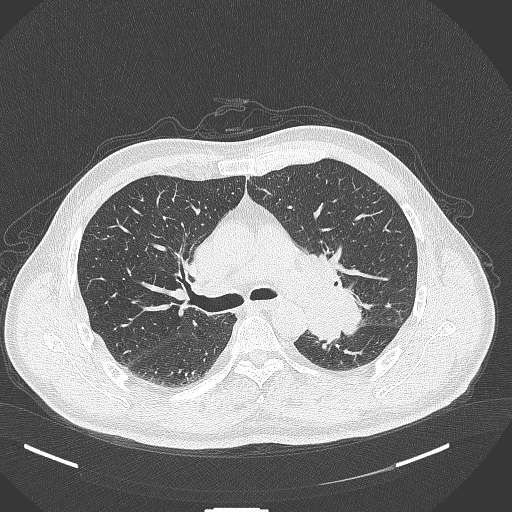
Chest CT, one axial slice; slice 263 of 429 in the series (ordered by position); 120 kVp; lung window (W 1500 / L -600 HU); 512 × 512 image matrix, field of view 400 × 400 mm. Patient: male, 55 years. From the clinical record (not read from this slice): clinical TNM (as recorded): T3 N0 M1c; histopathological grade: G3.
Structures marked on this image (rectangle marked by the reading radiologist):
- lung tumour (recorded histology: adenocarcinoma): bounding box (x1, y1, x2, y2) in pixels: (303, 282, 371, 348)